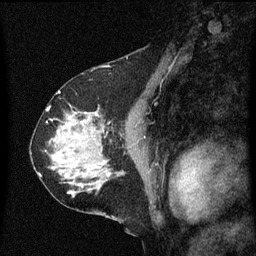
Breast MRI (dynamic contrast-enhanced), one sagittal slice. Slice 36 of 60 in the series (ordered by position). Dynamic contrast-enhanced series, image 2 of 3 at this slice position (ordered by acquisition). 1.5 T. TE 4.2 ms, TR 8 ms. 256 × 256 image matrix, field of view 200 × 200 mm. Female patient, age 58 years.
Structures marked on this image (semi-automatic segmentation, software-assisted and operator-edited):
- analysis volume of interest (the breast-tissue region the enhancement analysis was run in; not a lesion): bounding box [x1, y1, x2, y2] px = [56, 112, 99, 149]
- tumour enhancement mask (voxels above the 70 % enhancement threshold inside the analysis volume of interest): [70, 112, 88, 125]